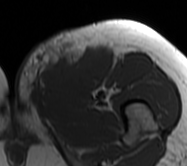
MRI of an extremity soft-tissue mass, one axial slice. Slice 19 of 62 in the series (ordered by position). MR volume resampled by the dataset authors to the PET/CT grid (not the native acquisition matrix). 3.27 mm slice thickness. 187 × 166 image matrix, field of view 183 × 162 mm. Female patient. Case-level facts recorded for this patient, not image findings: histological type: leiomyosarcoma; grade: high; site of the primary tumour: groin.
Annotated regions visible in this slice (expert contour drawn on MRI and transferred to this co-registered scan by the dataset authors):
- gross tumour volume including surrounding oedema: bounding box [x1, y1, x2, y2] px = [14, 37, 113, 111]
- gross tumour volume (mass): [39, 49, 111, 95]